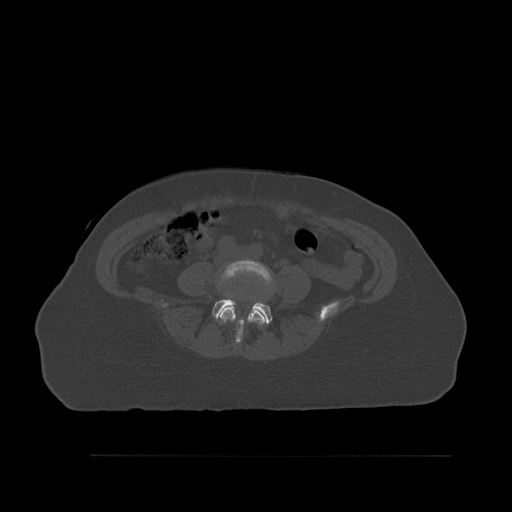
CT including the spine, one axial slice. Position 198 of 527 along the scan axis. Bone window (W 1800 / L 400 HU). 1.5 mm slice thickness. 512 × 512 image matrix, field of view 470 × 470 mm. Female patient, age 73 years. Case-level facts recorded for this patient, not image findings: primary cancer: breast; vertebrae with lytic lesions (as recorded): L2.
Outlined on this slice (semi-automatically segmented with operator editing):
- L4 vertebra: bounding box (x1, y1, x2, y2) in pixels: (218, 259, 274, 345)
- L5 vertebra: (212, 299, 273, 325)